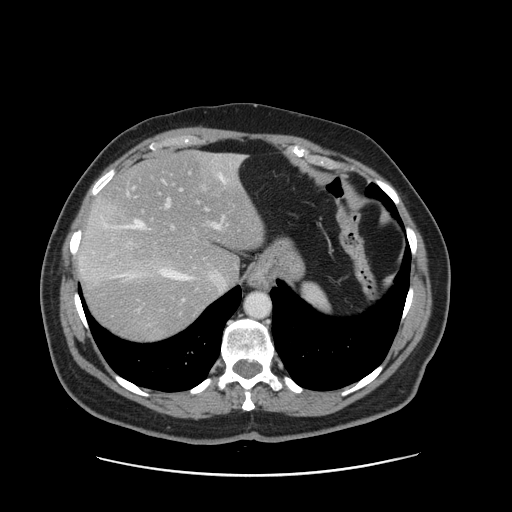
Contrast-enhanced abdominal CT, one axial slice. Position 118 of 161 along the scan axis. 120 kVp. Intravenous contrast given. Soft-tissue window (W 400 / L 40 HU). 512 × 512 image matrix, field of view 398 × 398 mm. Female patient, age 62 years. From the clinical record (not read from this slice): diagnosis: colorectal cancer liver metastases, imaged before liver resection; multiple liver metastases: no; largest metastasis: 2.5 cm; chemotherapy before resection: yes.
Outlined on this slice (outlined manually by an expert reader):
- hepatic veins: bounding box [x1, y1, x2, y2] px = [104, 156, 242, 281]
- liver: [77, 152, 265, 342]
- planned liver remnant (the part of the liver to remain after resection): [95, 152, 264, 283]
- portal vein (with intrahepatic branches): [164, 186, 224, 230]